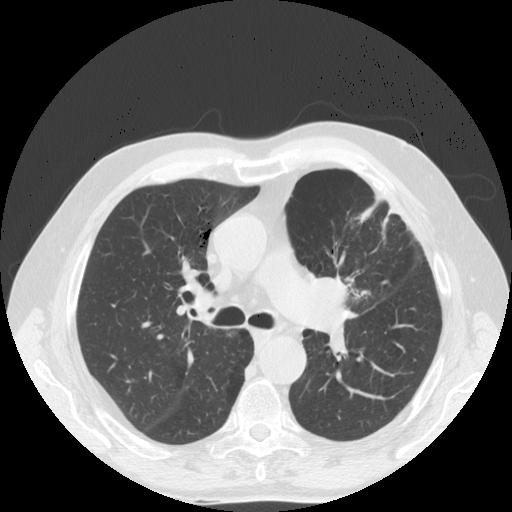
Low-dose screening chest CT, axial slice. Baseline screening round. Lung window (W 1500 / L -600 HU). 2.5 mm slice thickness. Slice 59 of 171 in the series. 512 × 512 image matrix. Male participant, aged 70 years at enrolment.
Expert-annotated lung lesion, box from (x=290, y=254) to (x=378, y=344) px. The exam's reader record, not a measurement of the box and not confirmed to be the same lesion: non-calcified nodule or mass ≥4 mm, left upper lobe, 46 × 31 mm, spiculated (stellate) margins, soft tissue attenuation. Official screen result: positive, change unspecified: nodule(s) >= 4 mm or enlarging nodule(s), mass(es), or other non-specific abnormalities suspicious for lung cancer. Lung cancer was diagnosed 78 days after this screen: squamous cell carcinoma, NOS, left upper lobe, poorly differentiated (G3), stage IIIB (AJCC 6th edition), 46 mm at pathology.